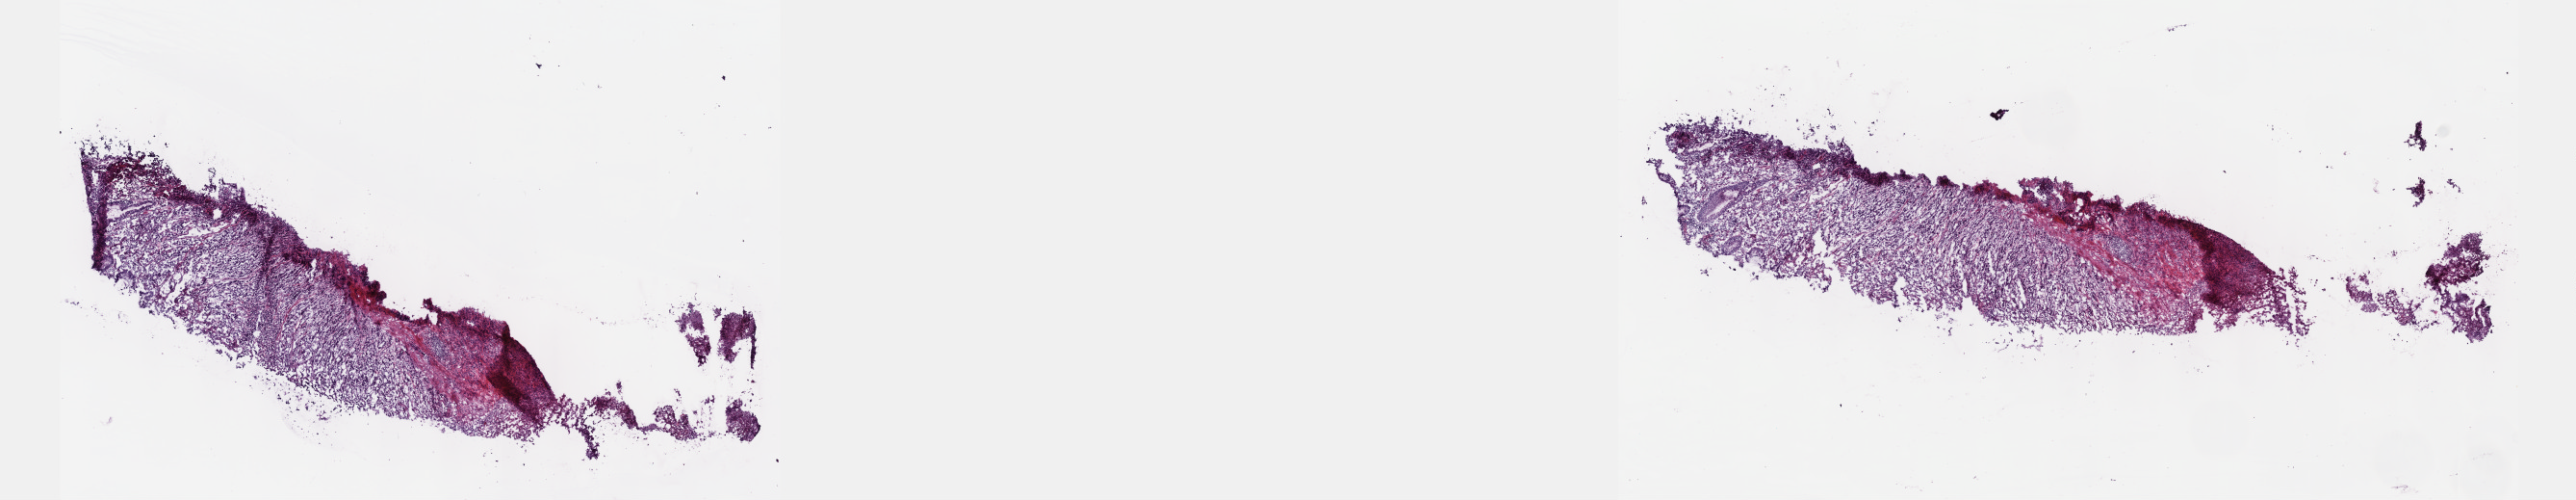
H&E whole-slide image, a low-resolution overview of the entire scanned area, about 21.6 x 4.2 mm; frozen section from the top of the tissue portion; stomach, primary tumour sample. Male patient; age at initial diagnosis 56 years. Histologic grade: G3 (poorly differentiated). Slide review estimates, as recorded: tumour cells 70%, tumour nuclei 70%, normal cells 4%, stromal cells 16%, necrosis 10%. Infiltration values recorded for this section: lymphocyte infiltration 3%, monocyte infiltration 2%, neutrophil infiltration 4%.
Diagnosis: Signet ring cell carcinoma (cardia, NOS). Lymph nodes positive (case pathology): 55 of 81 examined. AJCC pathologic stage: IV (6th edition).